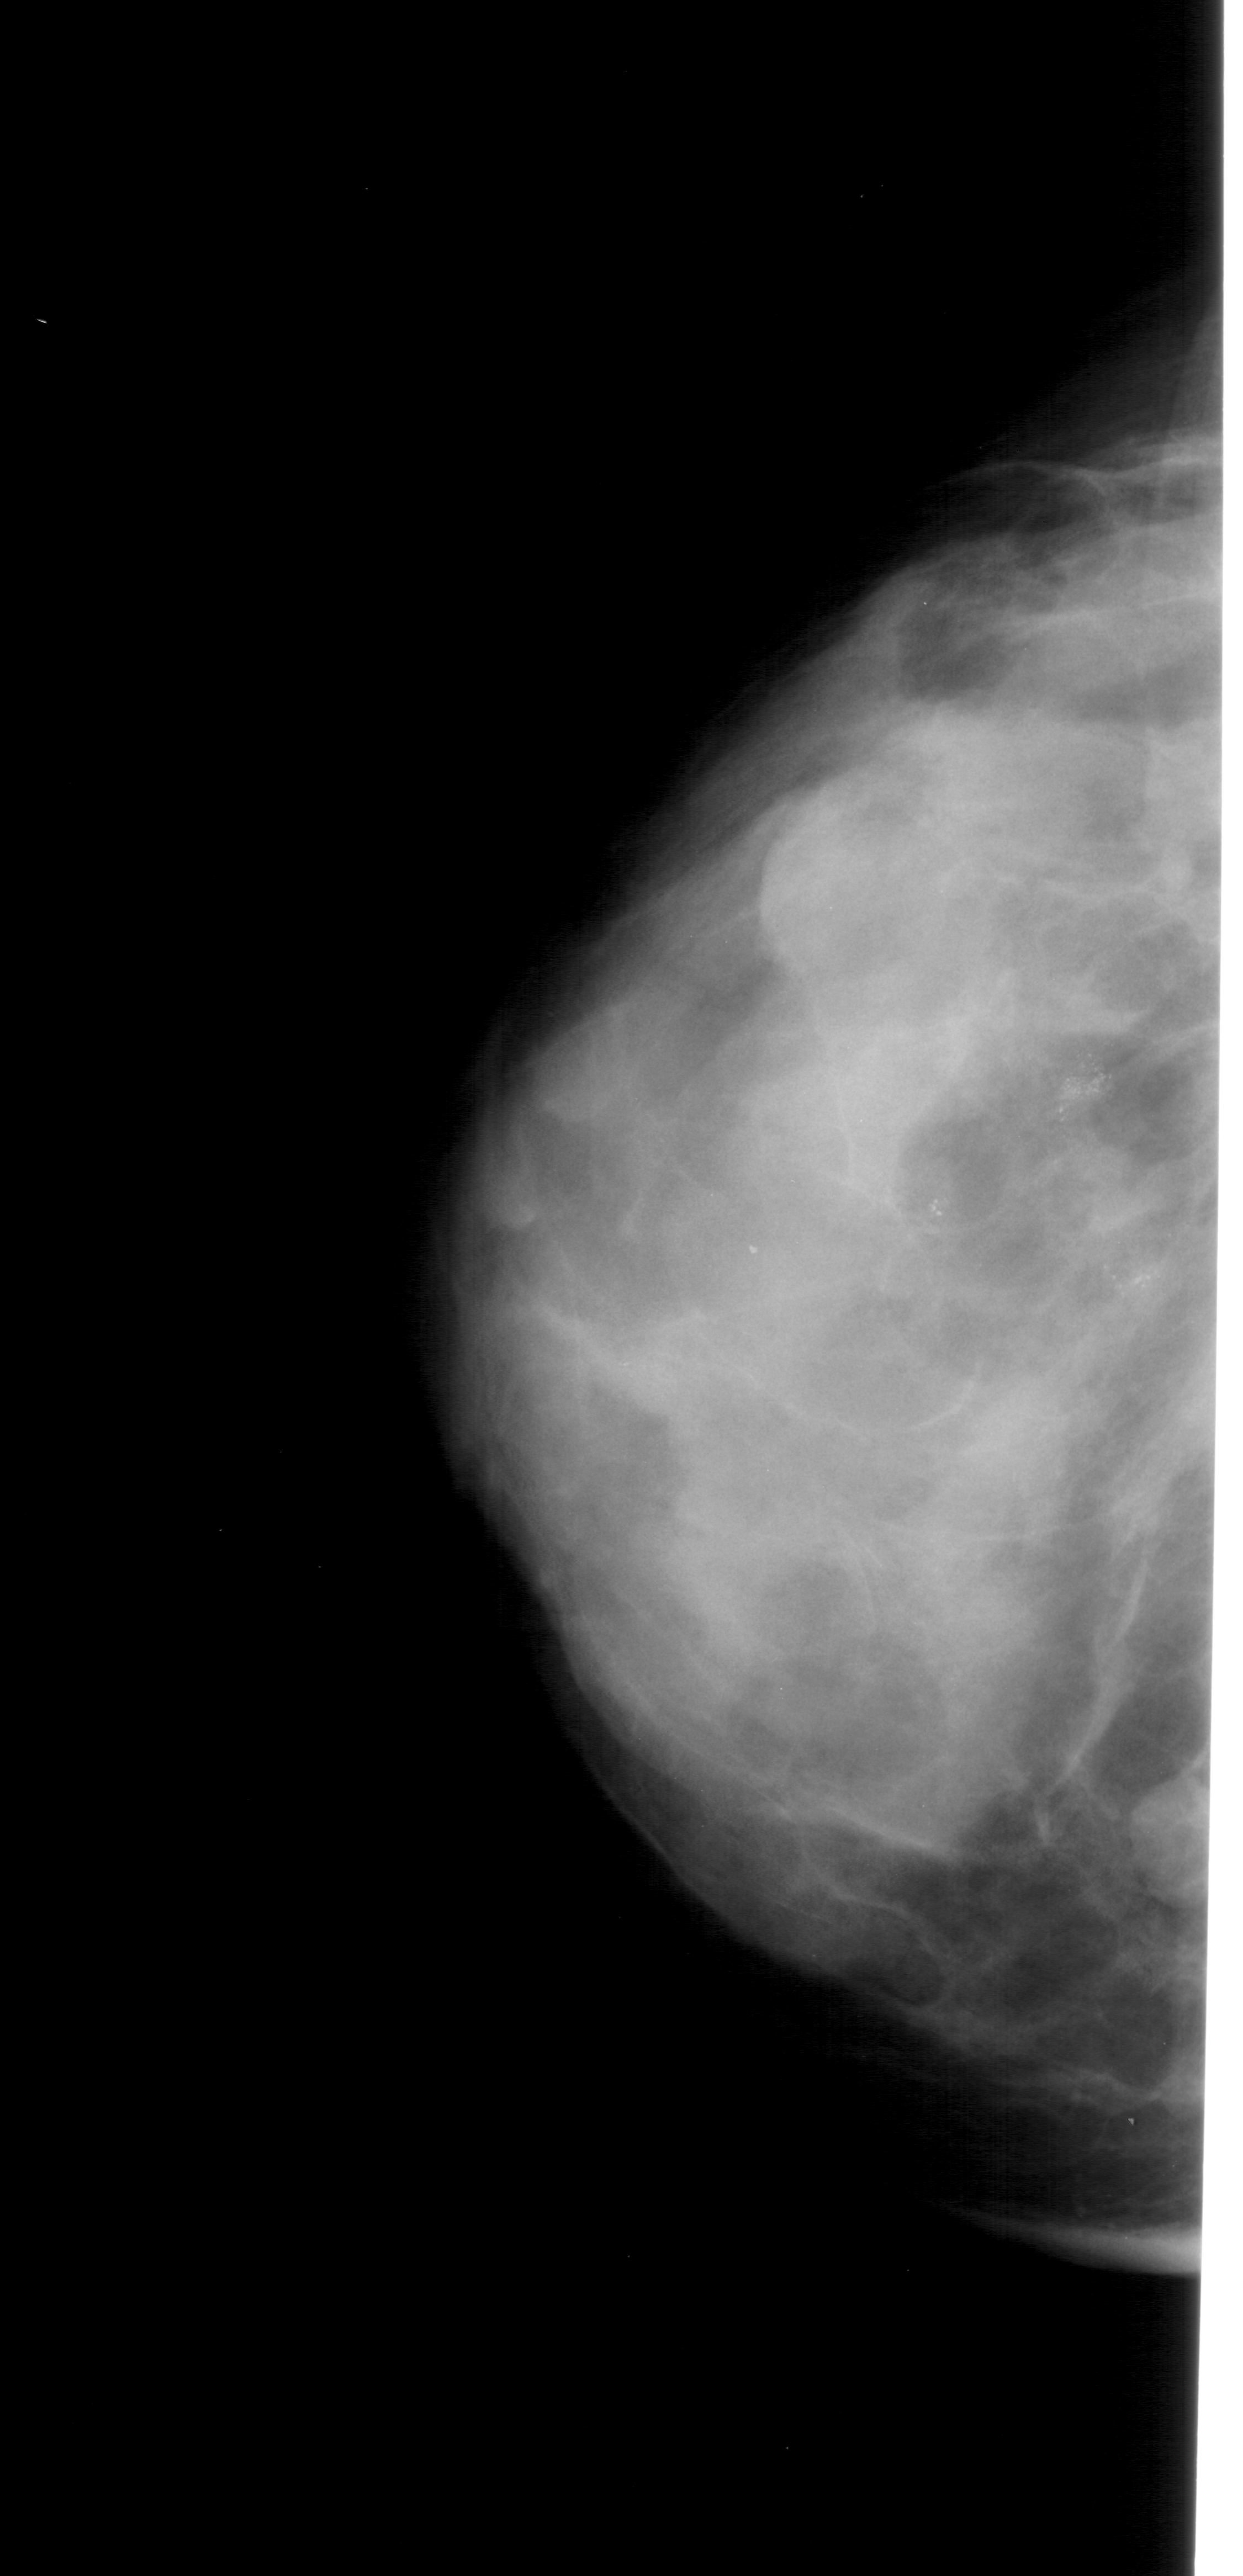
Scanned film-screen mammogram. Left breast. CC view. Breast composition: extremely dense (BI-RADS density category 4 of 4). 1243 × 2576 image matrix.
Expert-marked regions of interest on this image (one box per marked abnormality):
- Finding 1 of 2: calcifications, morphology pleomorphic, distribution clustered; BI-RADS assessment category 4; subtlety rating 3 on a 1 (subtle) to 5 (obvious) scale; pathology (as recorded): malignant: bounding box <1047,1029,1128,1136> (left, top, right, bottom; pixels)
- Finding 2 of 2: calcifications, morphology pleomorphic, distribution clustered; BI-RADS assessment category 4; pathology result (as recorded, not read from the image): malignant: <1100,1227,1186,1317>